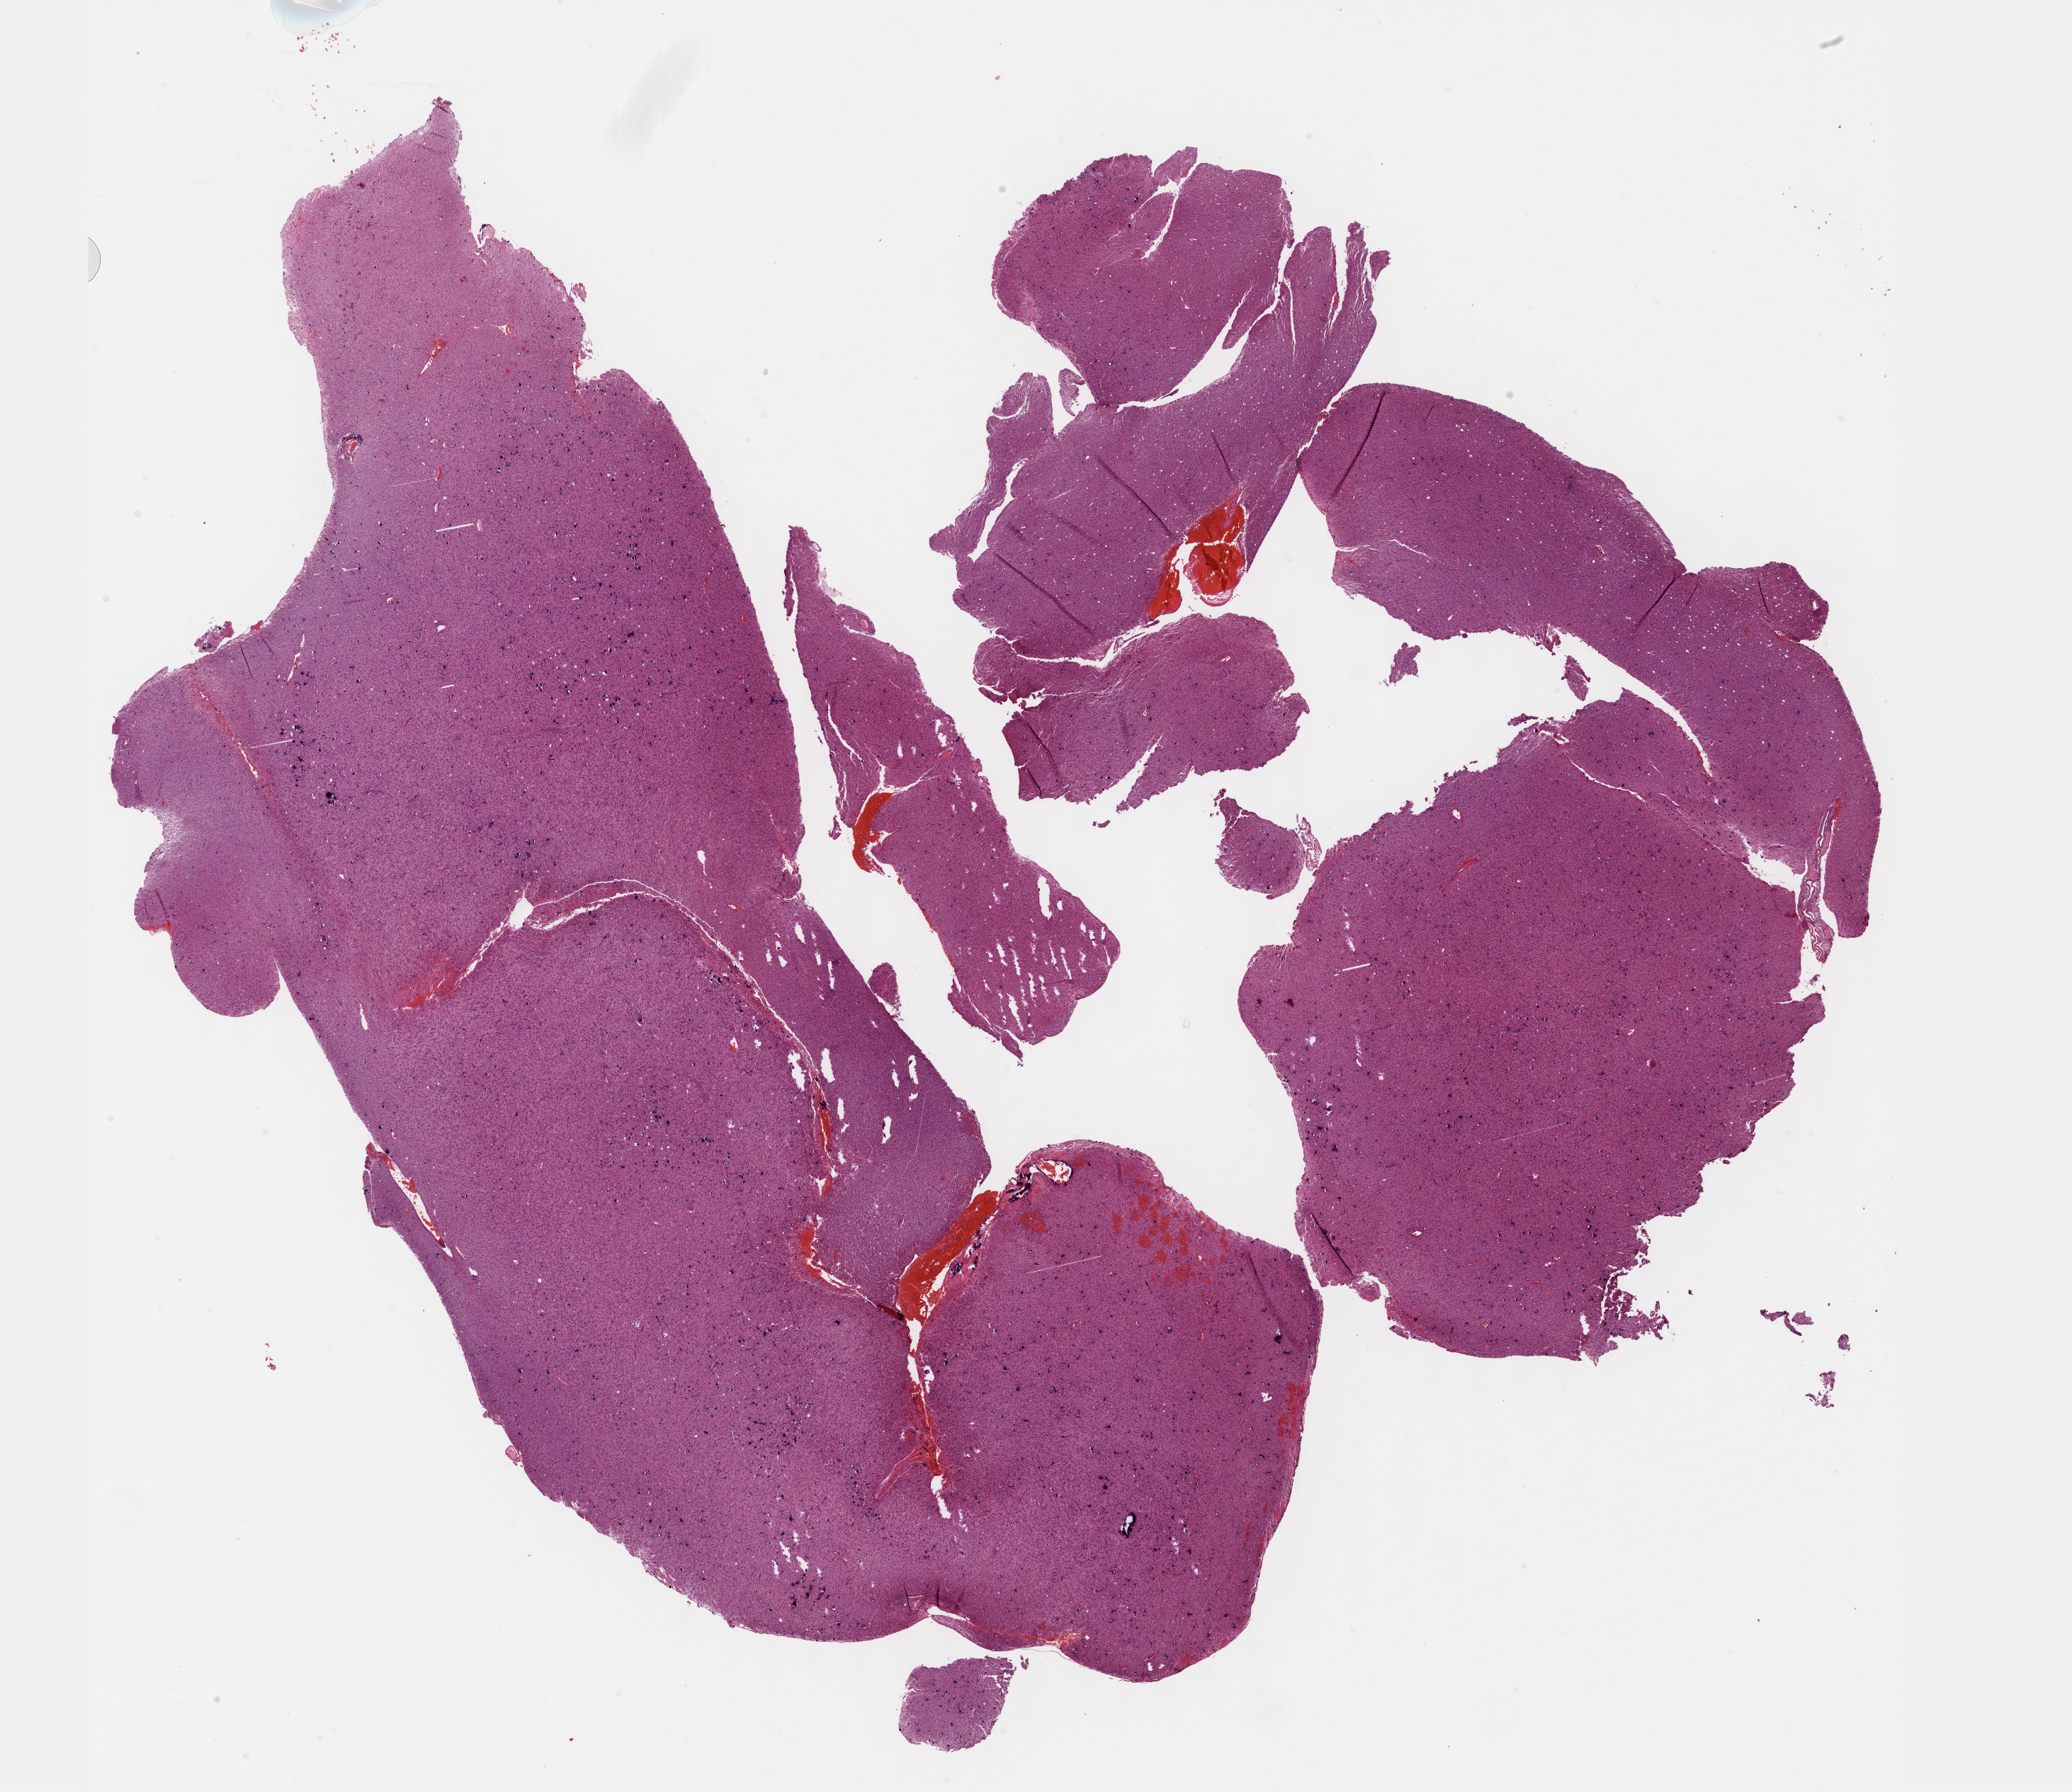
Whole-slide histology image, Hematoxylin and eosin (H&E) stained — whole scanned area (about 23.6 x 20.4 mm, from a 40x scan) shown as a low-resolution overview. FFPE section. Sample: primary tumour, brain. Female patient; age at initial diagnosis 60 years. Histologic grade: G3 (poorly differentiated).
Histologic diagnosis: Astrocytoma, anaplastic (cerebrum).